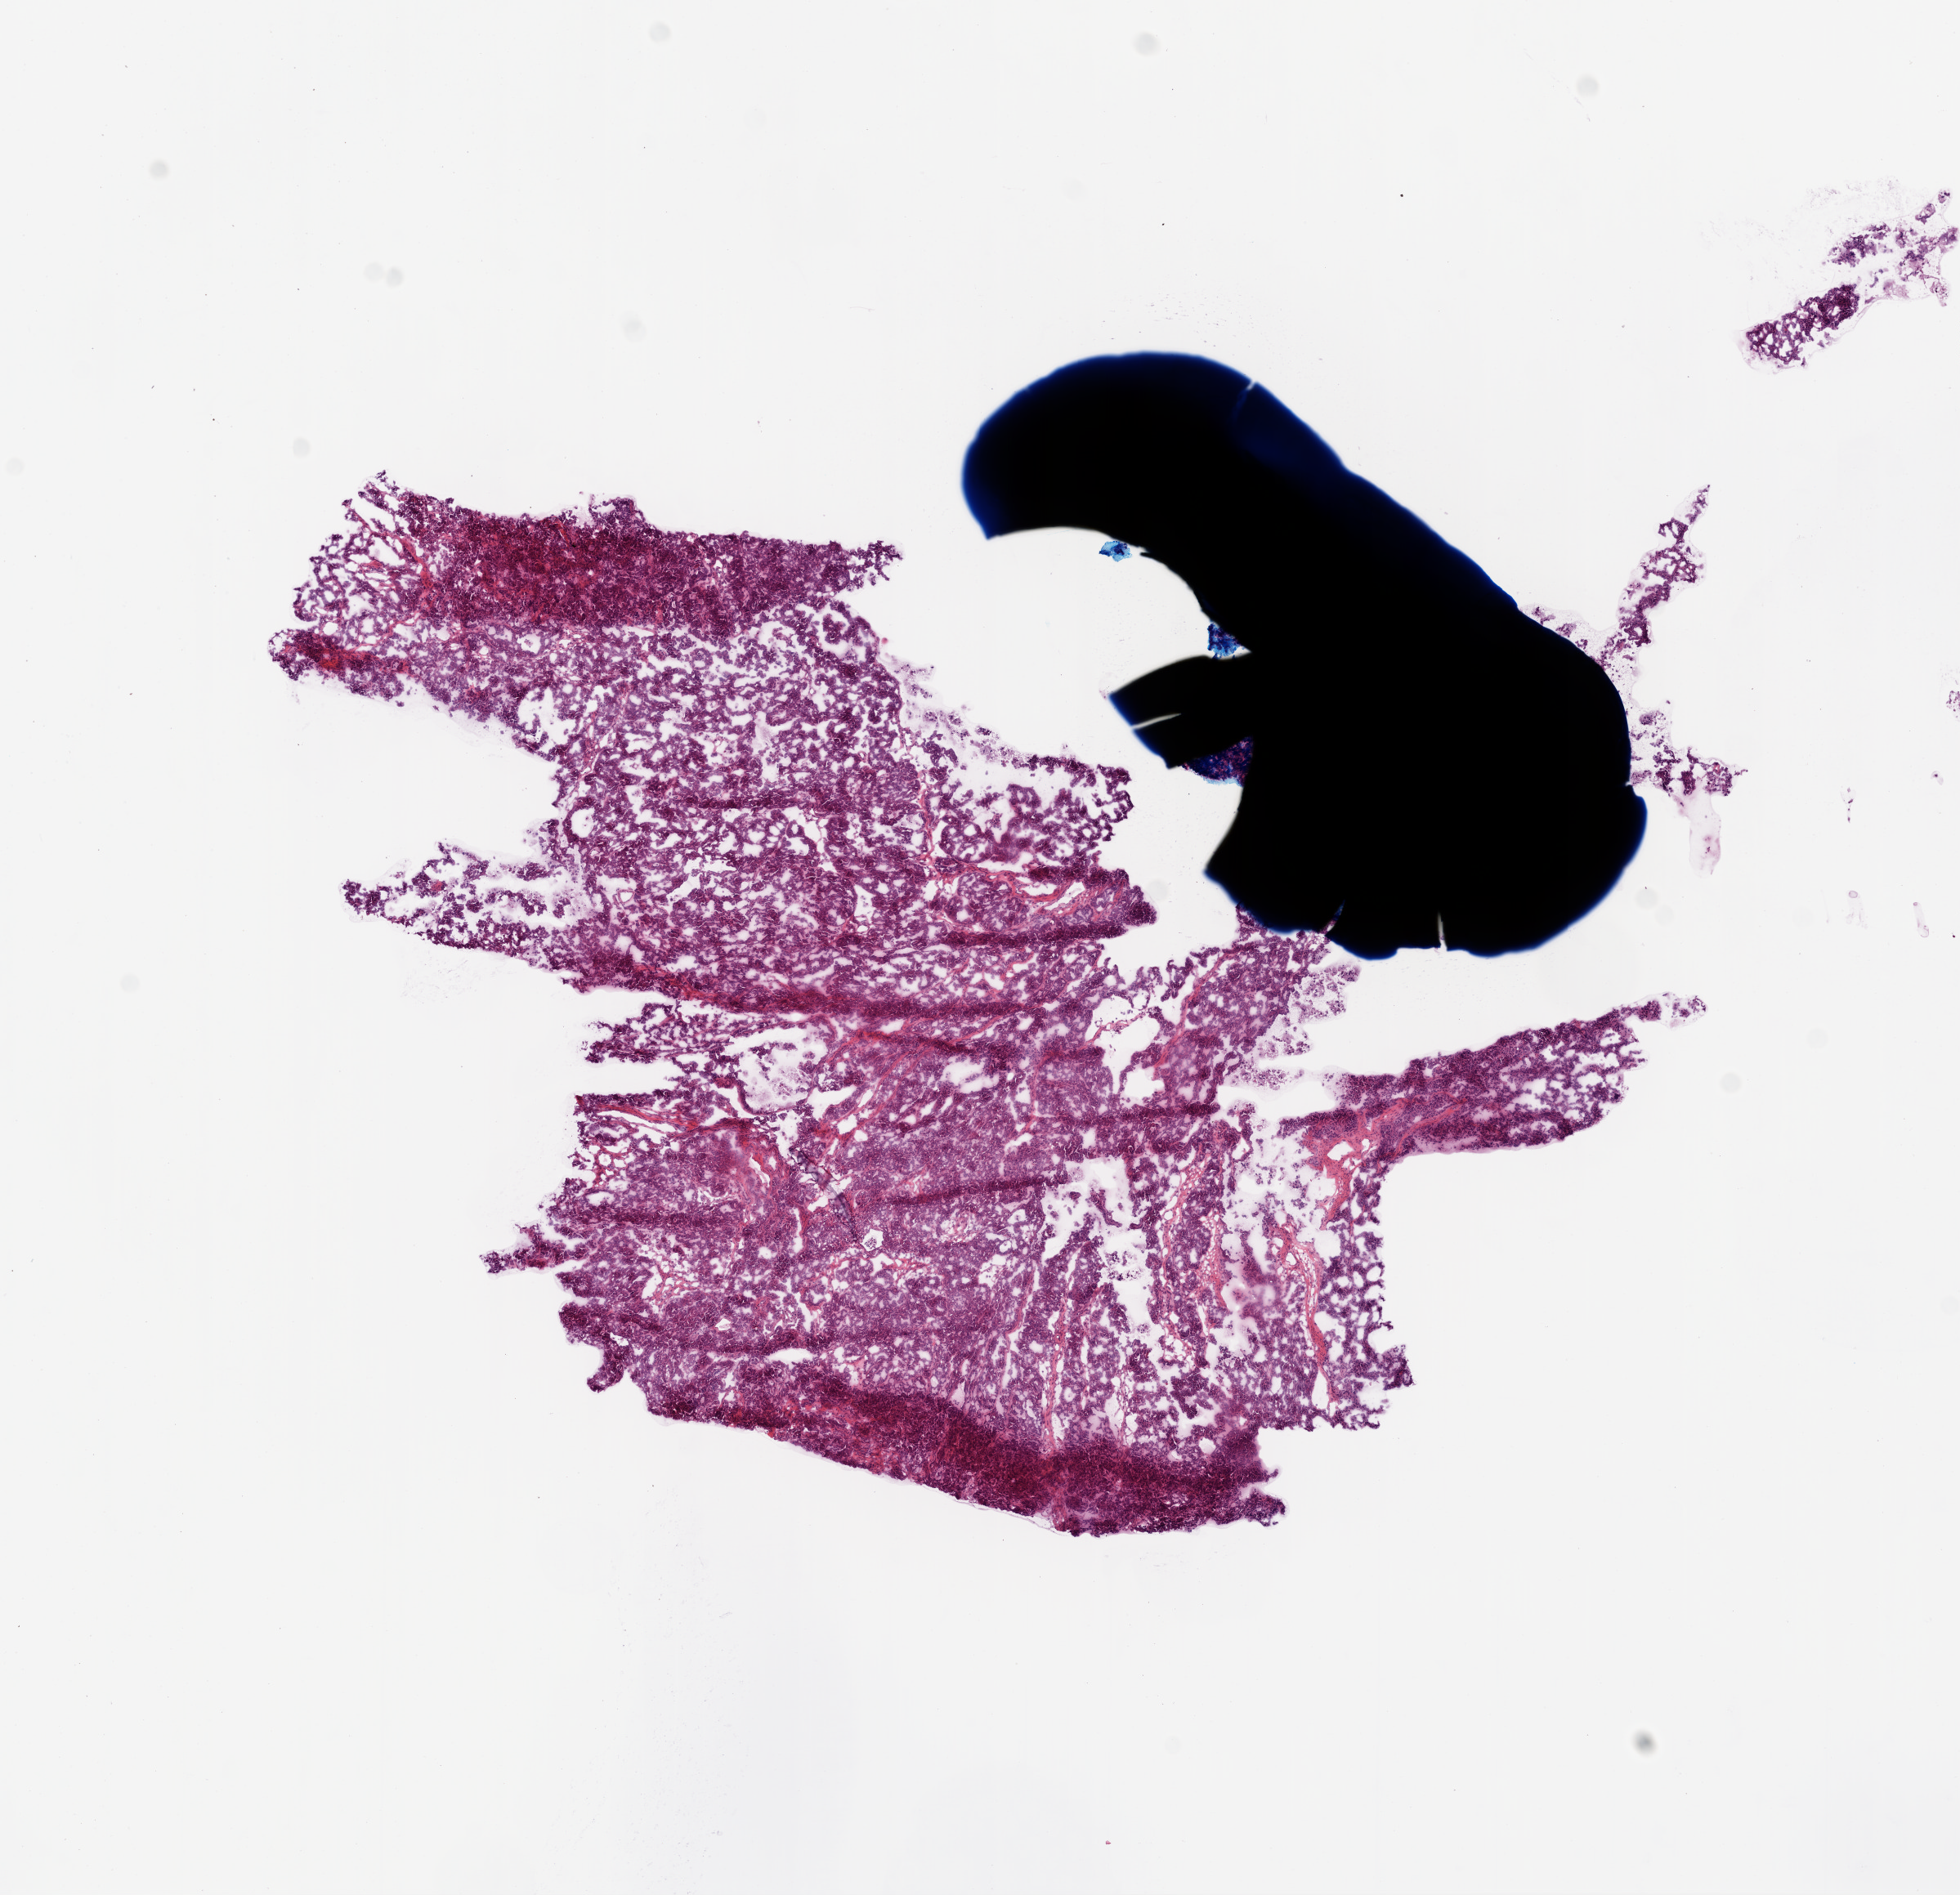
Whole-slide histology image, H&E, a low-resolution overview of the entire scanned area, about 9.7 x 9.4 mm (slide scanned at 20x). Frozen section from the top of the tissue portion. Primary tumour sample from the ovary. Patient: female, age at initial diagnosis 69 years. Histologic grade: G3 (poorly differentiated). Slide review estimates, as recorded: tumour cells 90%, tumour nuclei 90%, normal cells 5%, stromal cells 5%, necrosis 0%.
Pathologic diagnosis: Serous cystadenocarcinoma, NOS. FIGO stage: IIIC.